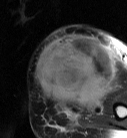
MRI of an extremity soft-tissue mass, one axial slice. T2-weighted fat-saturated. MR volume resampled by the dataset authors to the PET/CT grid (not the native acquisition matrix). 3.27 mm slice thickness. 127 × 138 image matrix, field of view 124 × 135 mm. Female patient. Case-level facts recorded for this patient, not image findings: histological type: pleiomorphic leiomyosarcoma; grade: high; site of the primary tumour: left biceps.
Annotated regions visible in this slice (expert contour drawn on MRI and transferred to this co-registered scan by the dataset authors):
- gross tumour volume including surrounding oedema: box from (x=36, y=34) to (x=115, y=108) px
- gross tumour volume (mass): (x=36, y=34)–(x=115, y=106)